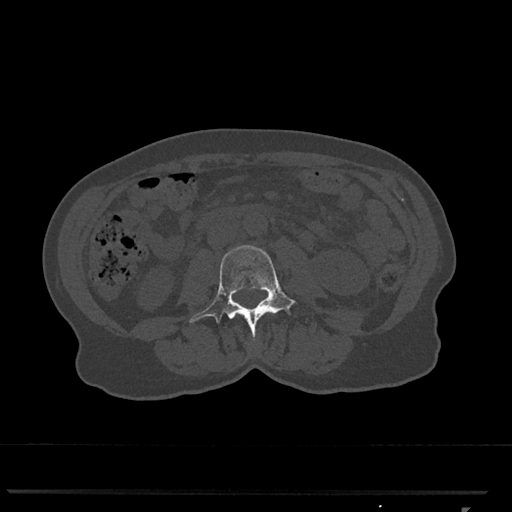
CT including the spine, one axial slice. Slice 276 of 793 in the series (ordered by position). 120 kVp. Bone window (W 1800 / L 400 HU). 512 × 512 image matrix, field of view 380 × 380 mm. Patient: female, 62 years. Case-level facts recorded for this patient, not image findings: primary cancer: renal.
Annotated regions visible in this slice (semi-automatic segmentation, software-assisted and operator-edited):
- L3 vertebra: bounding box (x1, y1, x2, y2) in pixels: (189, 245, 296, 338)